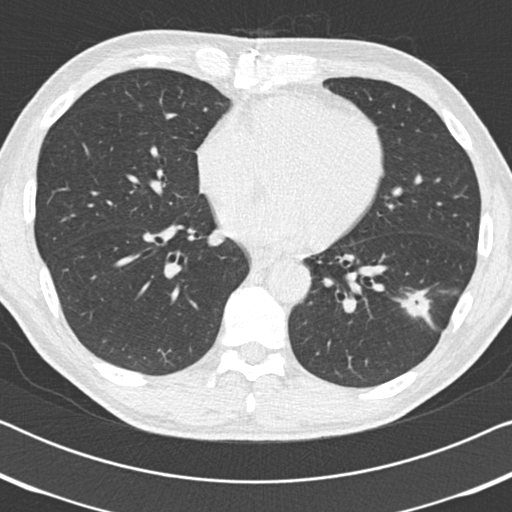
Chest CT (low-dose screening protocol), one axial image. Third screening round (two years after baseline). Lung window (W 1500 / L -600 HU). Standard (soft-tissue) reconstruction kernel (B30f). Slice 109 of 186 in the series. 512 × 512 image matrix, field of view 330 × 330 mm. Male participant, aged 59 years at enrolment. Current smoker at enrolment.
- Lesion marked by an expert reader, bounding box [x1, y1, x2, y2] px = [388, 275, 455, 338].
- The screening reader recorded 2 non-calcified nodules or masses ≥4 mm on this exam (left lower lobe, right middle lobe); which of them this box marks is not recorded.
- Official screen result: positive, other.
- Participant outcome: lung cancer diagnosed 73 days after this screen — adenocarcinoma, NOS, left lower lobe, poorly differentiated (G3), stage IA (AJCC 6th edition), 20 mm at pathology.